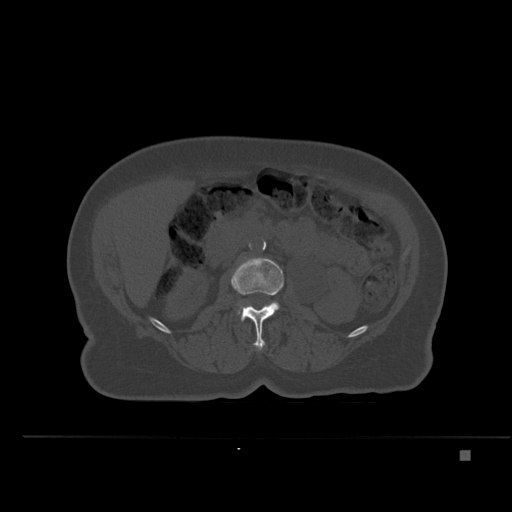
CT including the spine, one axial slice. Slice 213 of 477 in the series (ordered by position). Bone window (W 1800 / L 400 HU). 1.5 mm slice thickness. 512 × 512 image matrix, field of view 422 × 422 mm. Patient: female, 74 years. From the clinical record (not read from this slice): primary cancer: colon.
Structures marked on this image (semi-automatically segmented with operator editing):
- L2 vertebra: bounding box <231,257,284,349> (left, top, right, bottom; pixels)